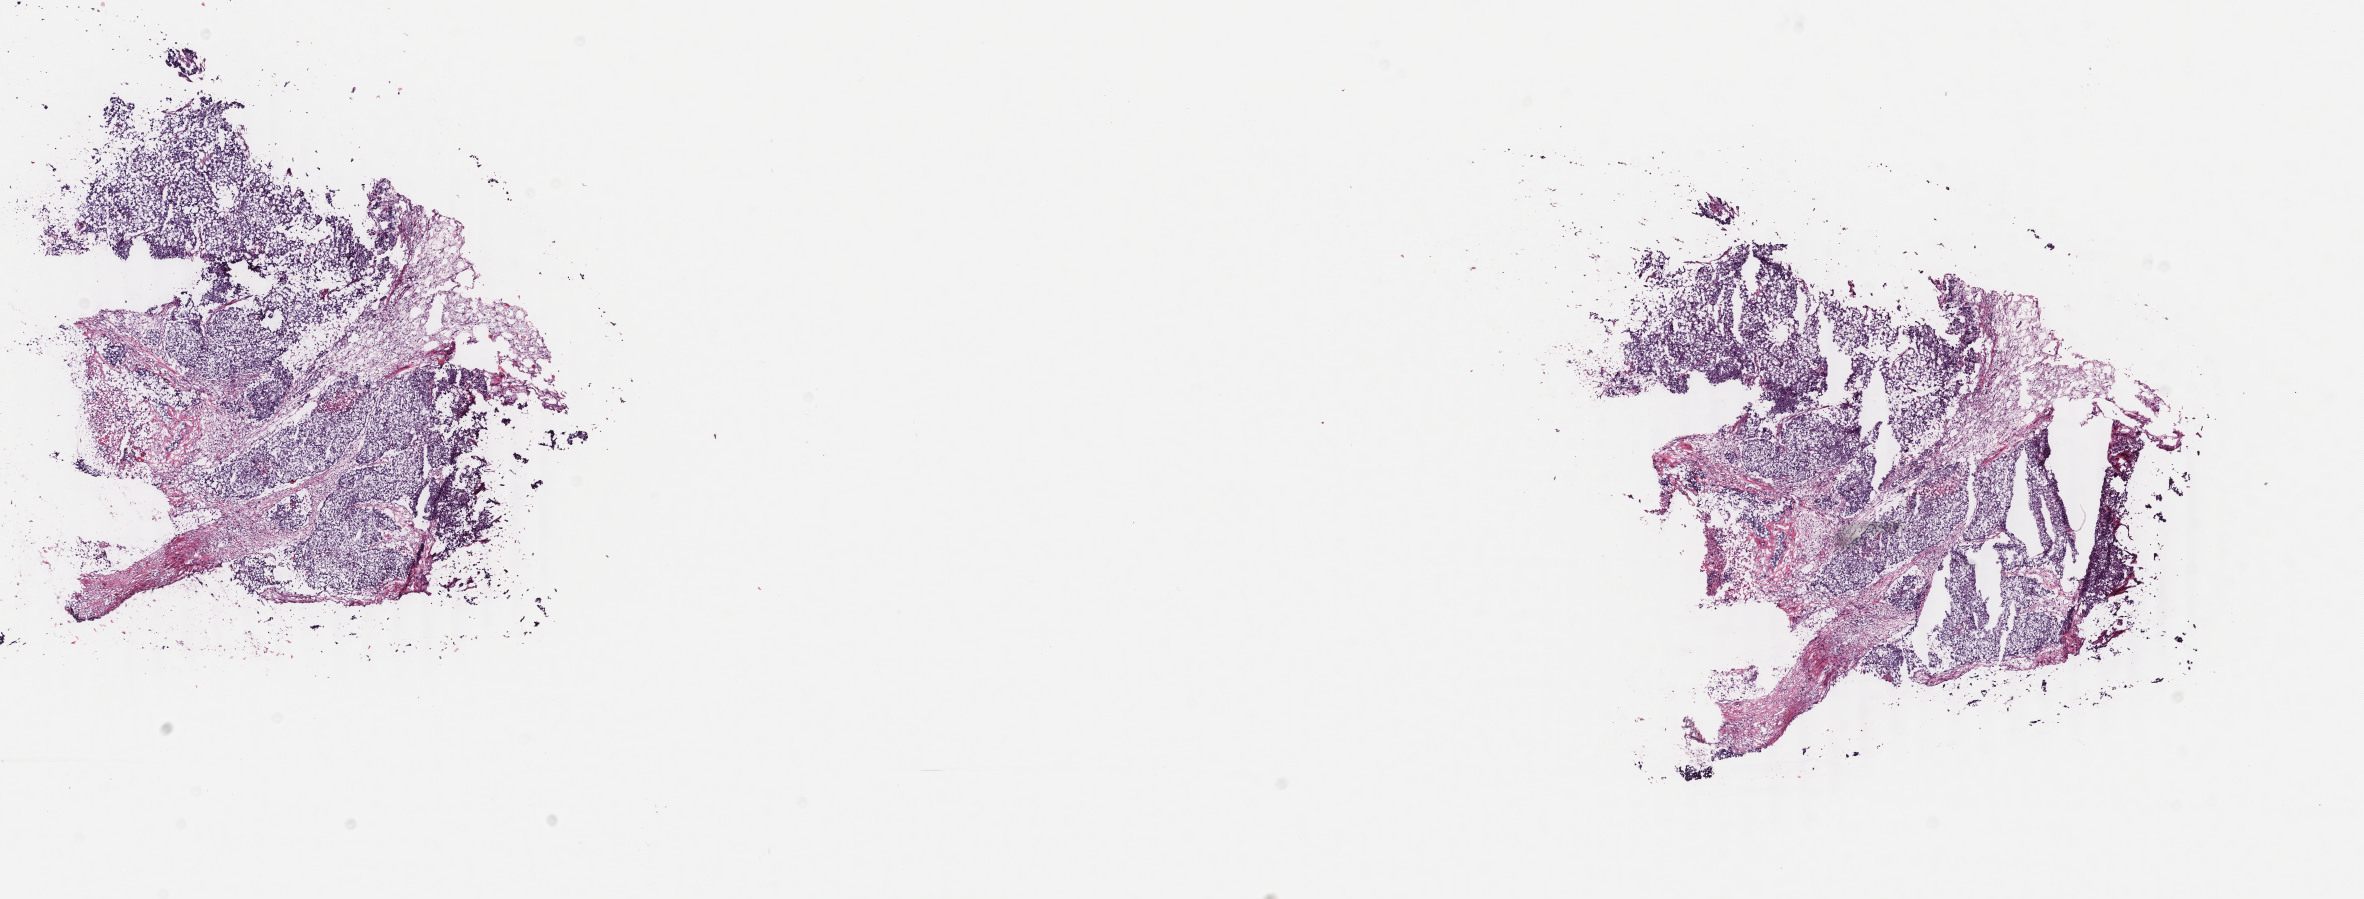
H&E-stained whole-slide image, shown as a low-resolution overview of the whole scanned area (about 18.8 x 7.1 mm); frozen section from the top of the tissue portion; breast, primary tumour sample. Patient: female, age at initial diagnosis 36 years. Composition of this section per pathologist review: tumour cells 85%, tumour nuclei 85%, normal cells 0%, stromal cells 13%, necrosis 2%. Infiltration values recorded for this section: lymphocyte infiltration 2%, monocyte infiltration 1%, neutrophil infiltration 0%.
- diagnosis: Infiltrating duct carcinoma, NOS
- lymph nodes positive (case pathology): 0 of 17 examined
- AJCC pathologic stage: IIA (6th edition)
- laterality: right